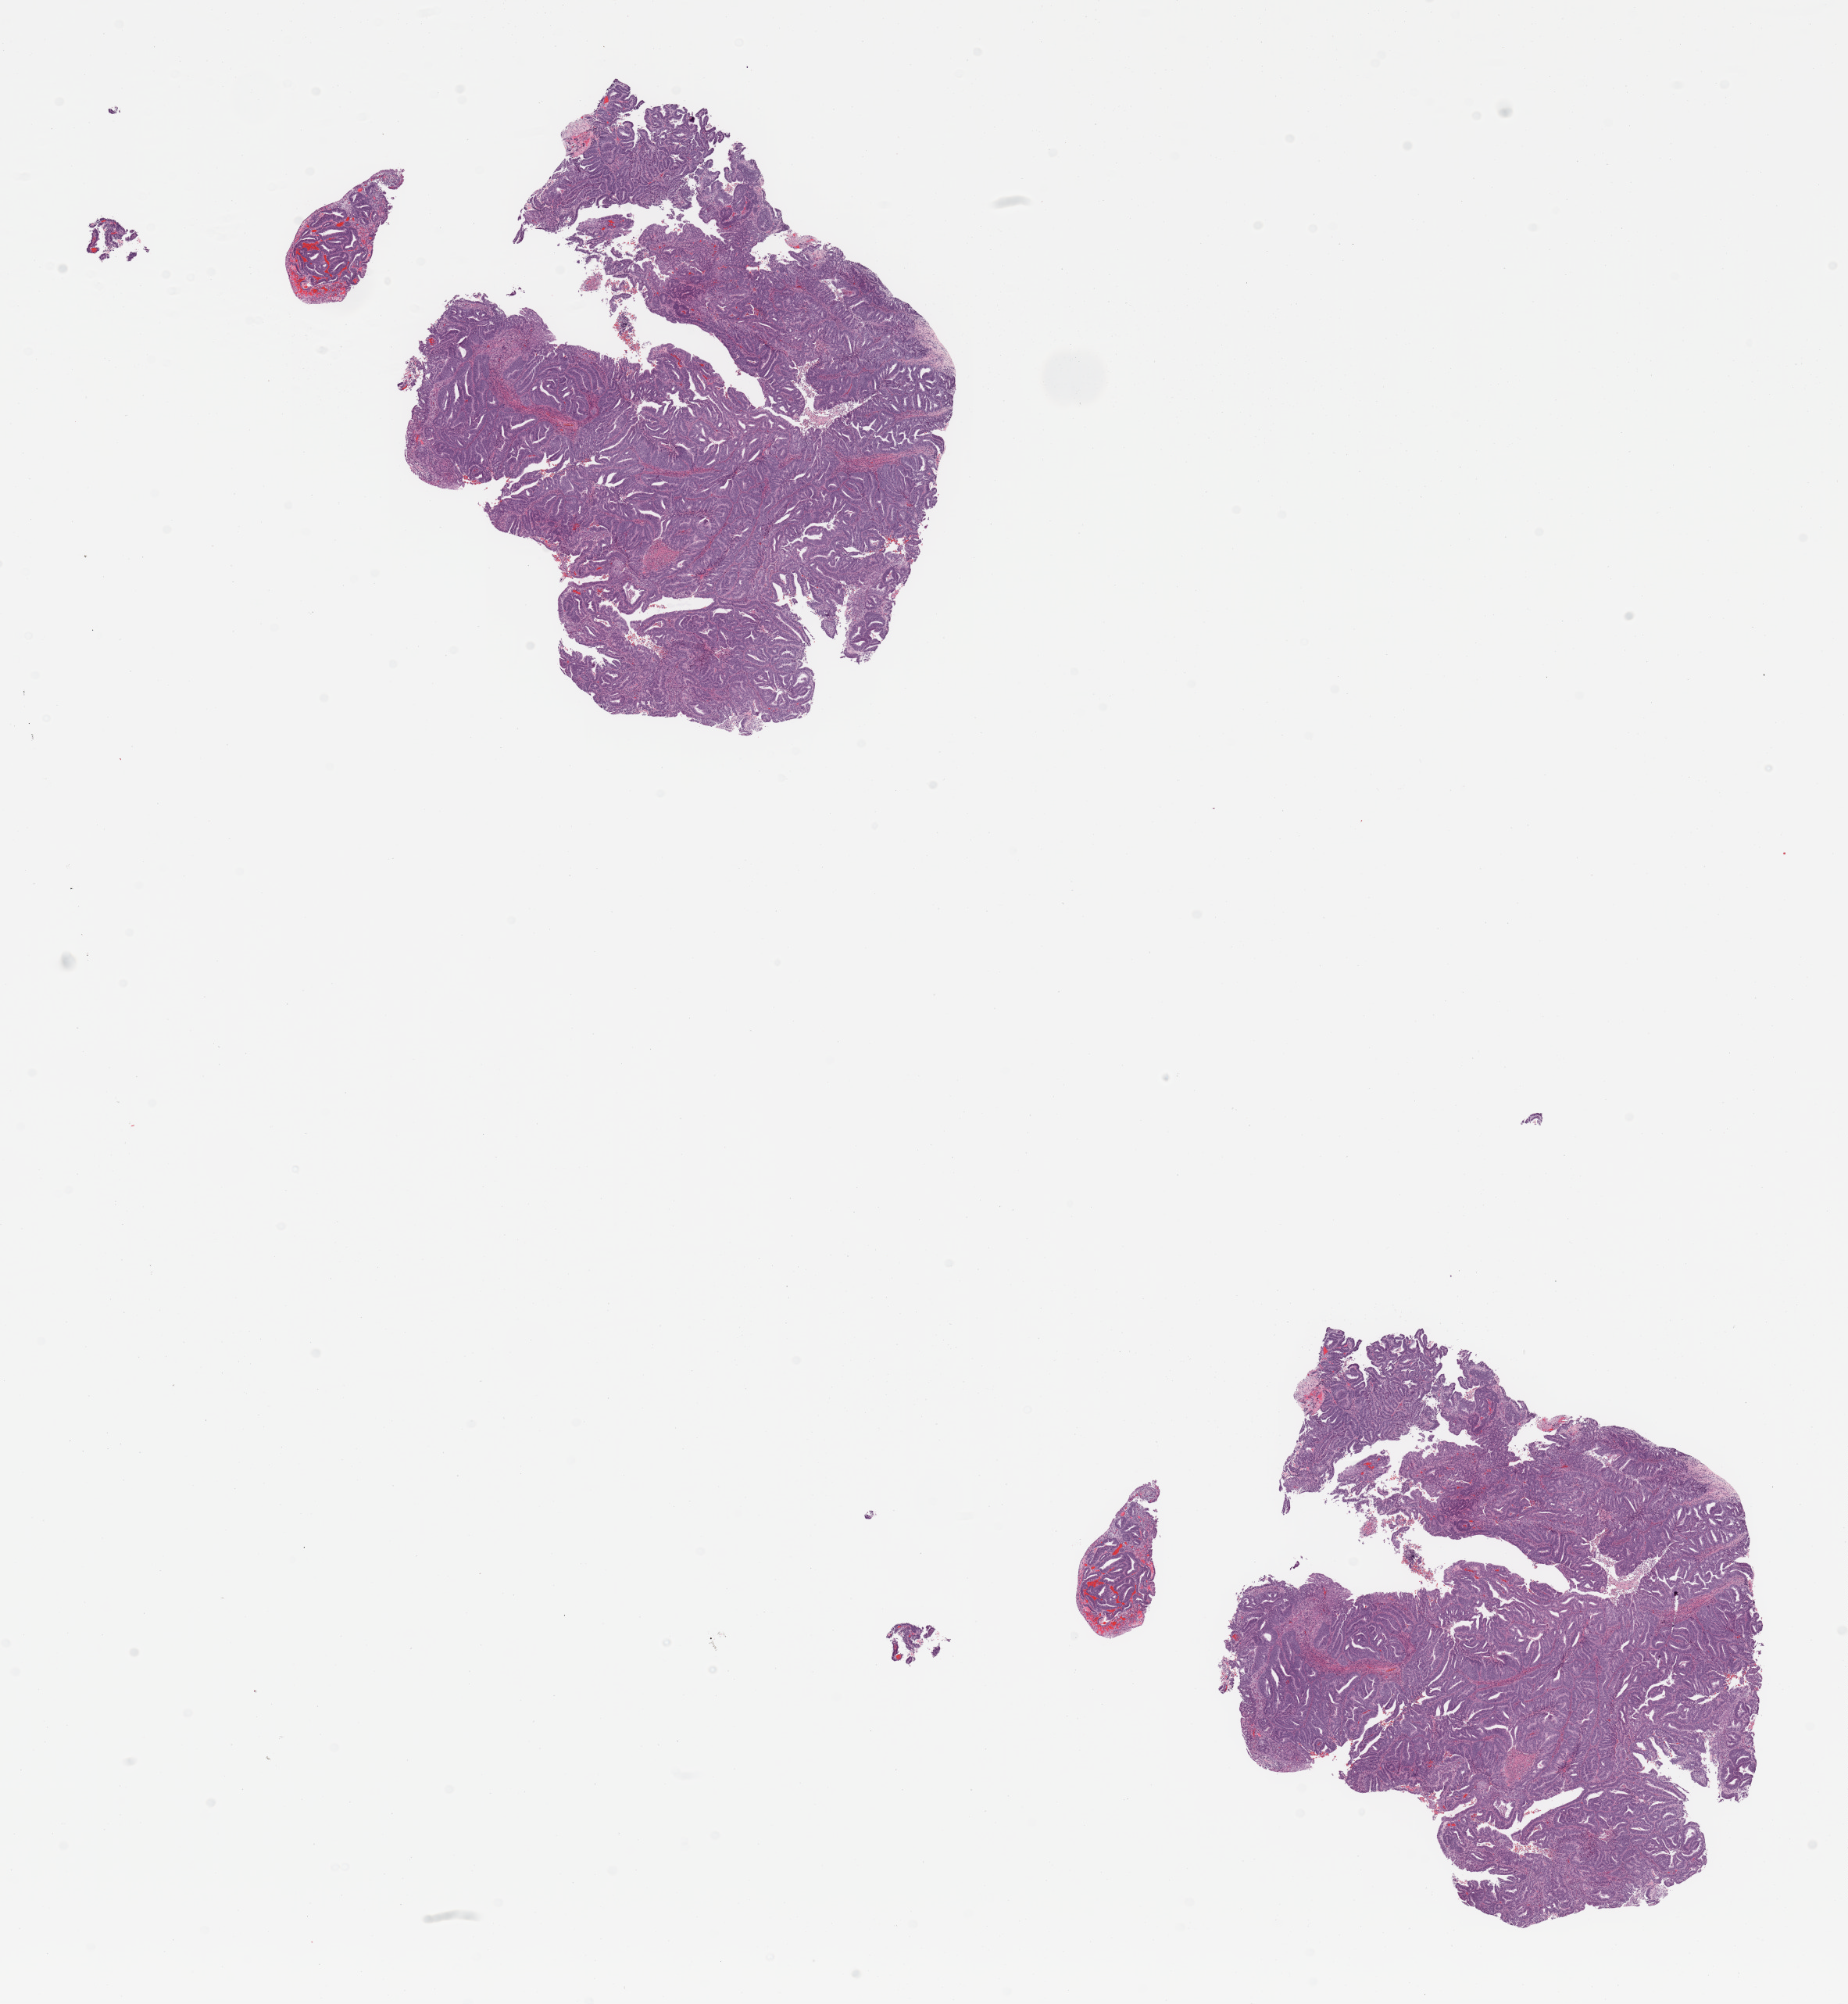
Whole-slide histology image, Hematoxylin and eosin (H&E) stained — low-resolution overview of the scanned area, about 18.7 x 20.3 mm. Tumour tissue sample, sampled site: uterus. Patient: female, age 60 years. Histologic grade: G1 (well differentiated). Pathologist review of this section (percent, as recorded): tumour nuclei 95%, necrosis 5%.
AJCC pathologic stage: I. Histologic diagnosis: Endometrioid adenocarcinoma, NOS.